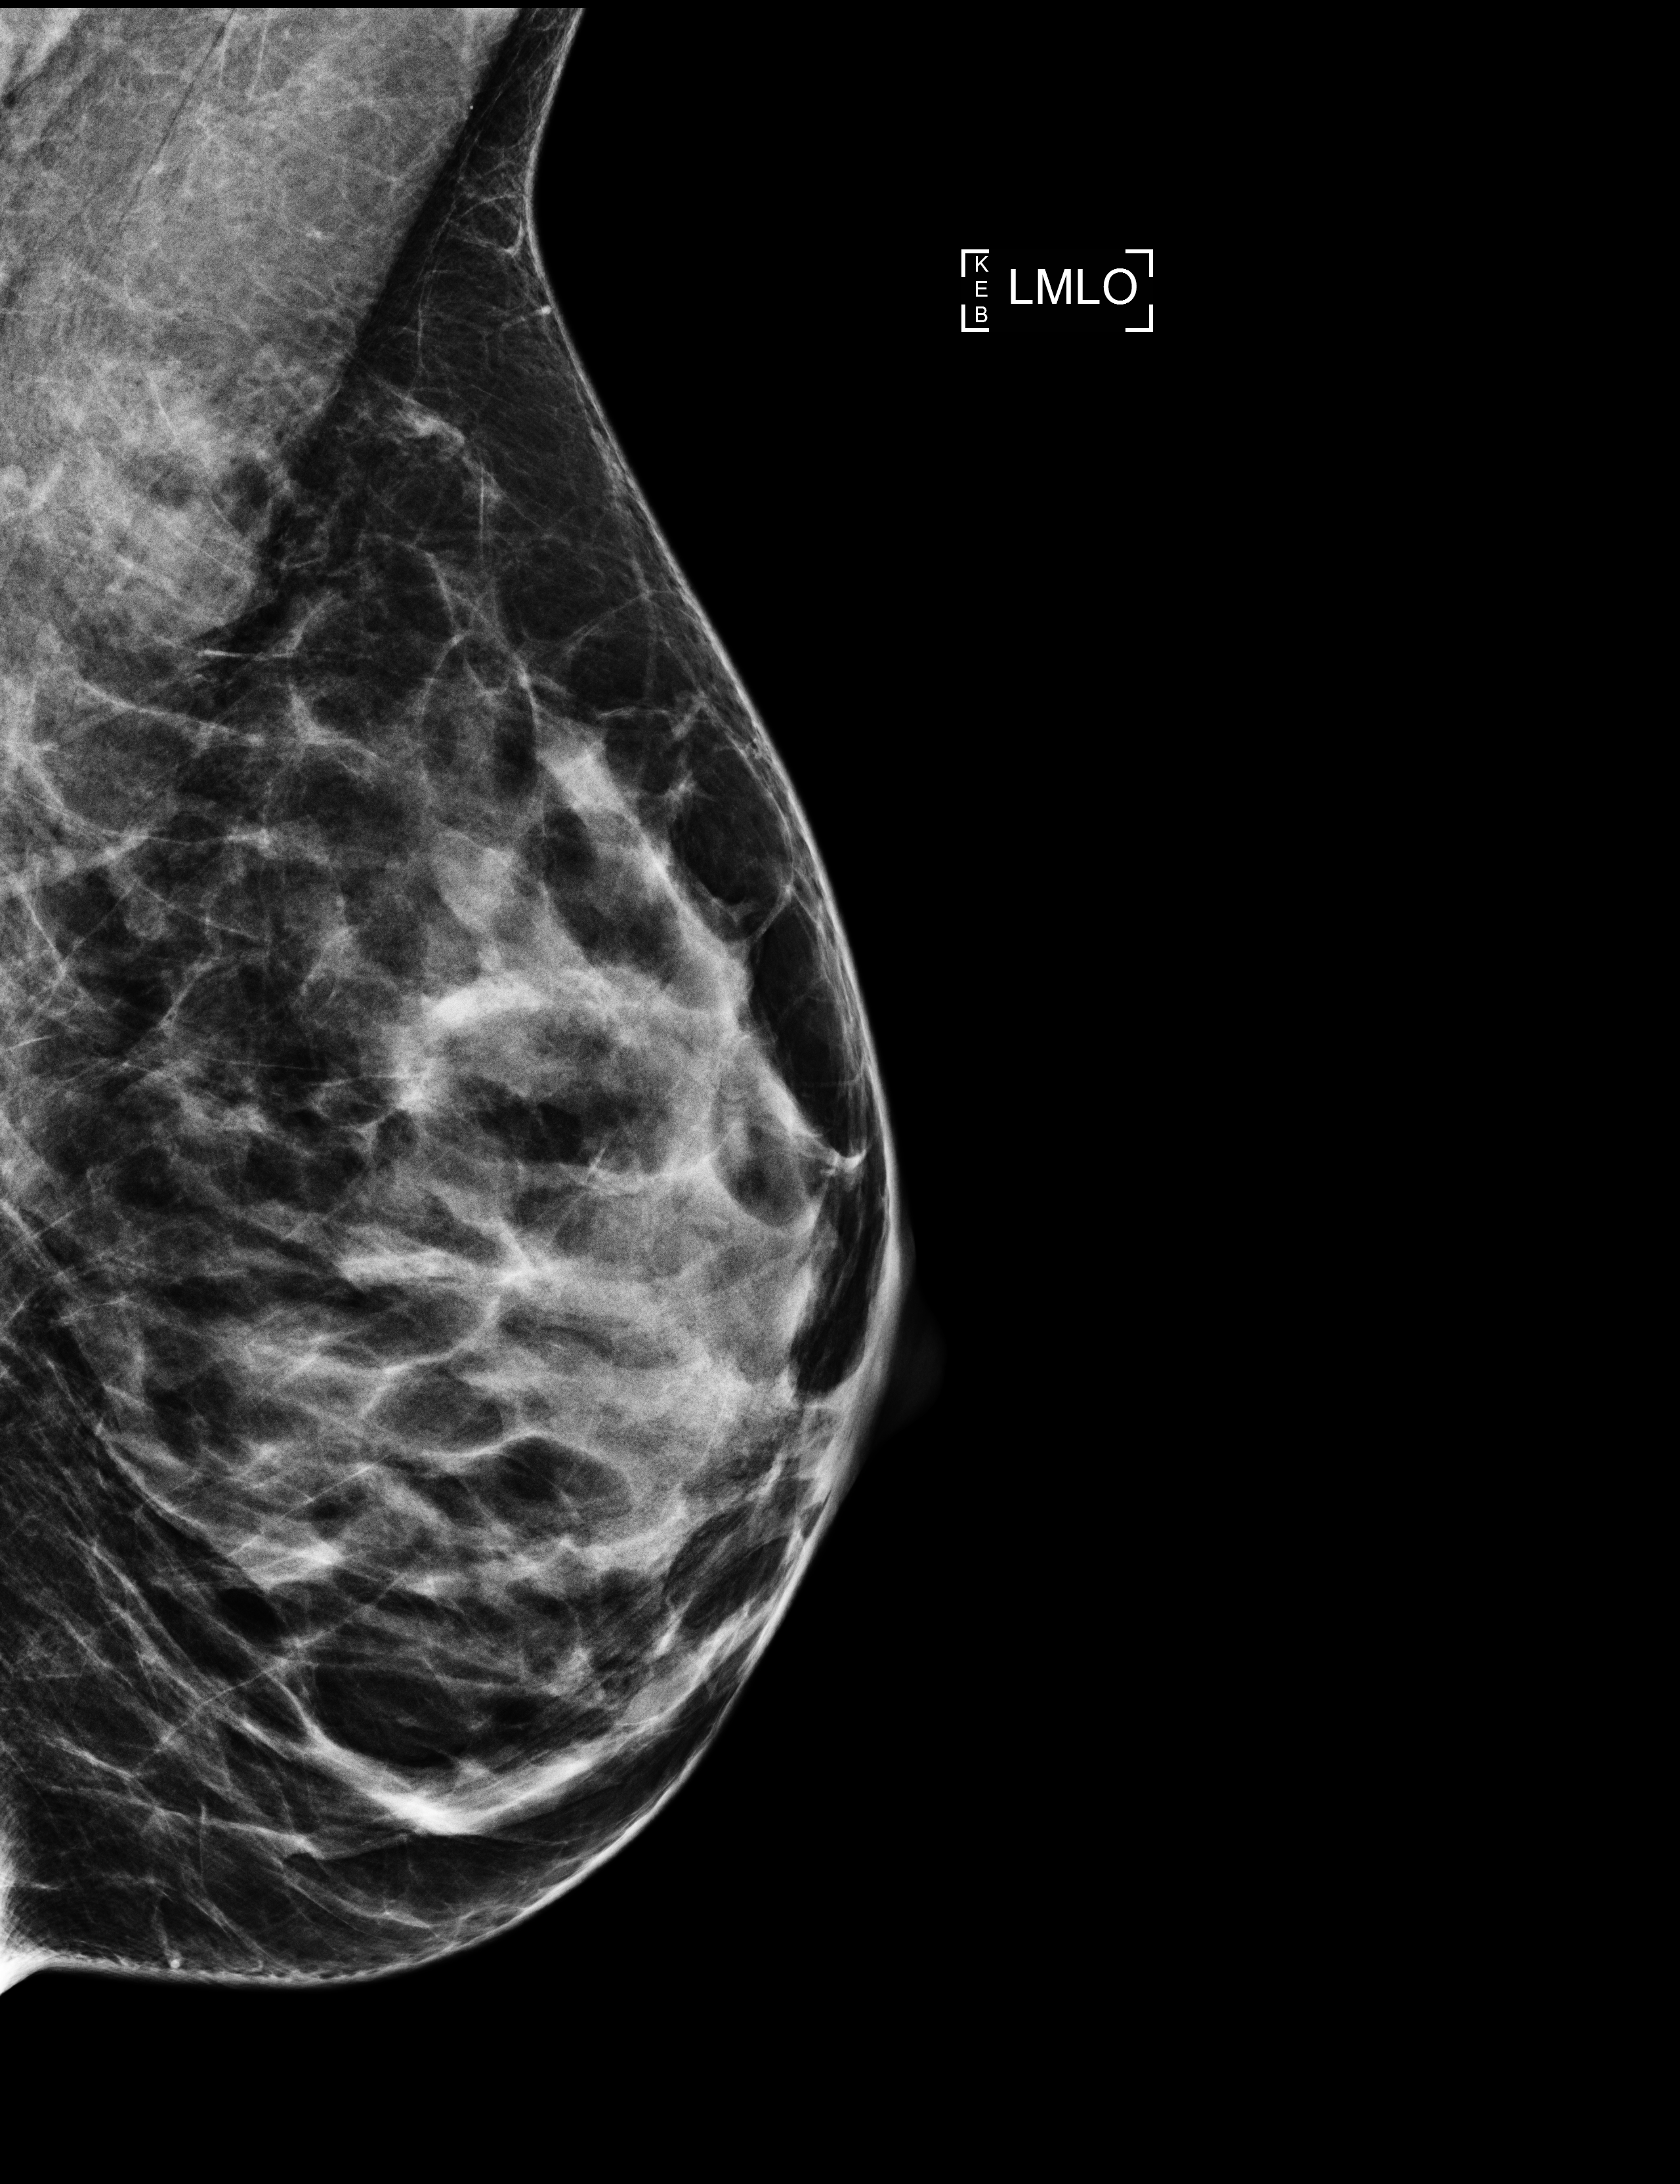
Diagnostic examination (additional views), system: Selenia Dimensions. Female patient, age 56 years.
Image type: full-field digital mammogram. Breast: left. Projection: mediolateral oblique (MLO) view.